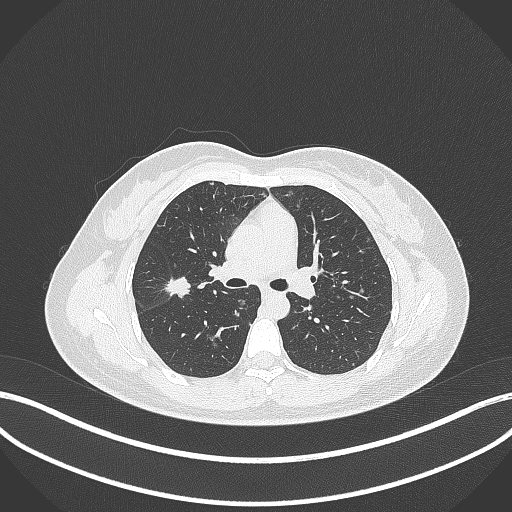
Chest CT, one axial slice. Position 205 of 307 along the scan axis. Reconstruction kernel B70f. 120 kVp. Lung window (W 1500 / L -600 HU). 1 mm slice thickness. 512 × 512 image matrix. Patient: female, 33 years. Case-level facts recorded for this patient, not image findings: clinical TNM (as recorded): T1c N0 M0; histopathological grade: G2-G3.
Annotated regions visible in this slice (bounding box drawn by a radiologist):
- lung tumour (recorded histology: adenocarcinoma): bounding box [x1, y1, x2, y2] px = [164, 275, 193, 302]